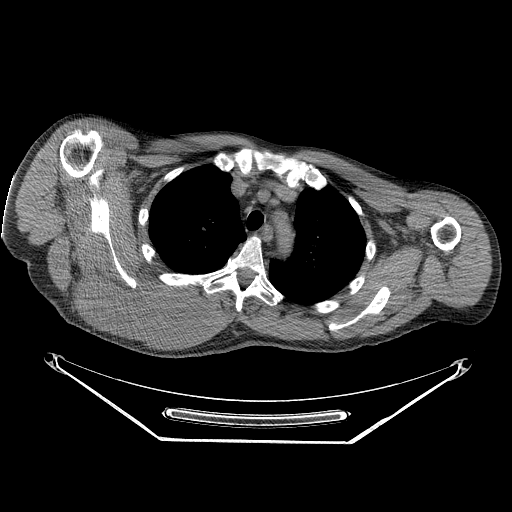
CT of an extremity soft-tissue mass (from a PET/CT study), one axial slice; slice 191 of 267 in the series (ordered by position); reconstruction kernel STANDARD; 140 kVp; soft-tissue window (W 400 / L 40 HU); 512 × 512 image matrix, field of view 500 × 500 mm. Male patient. Case-level facts recorded for this patient, not image findings: histological type: pleiomorphic spindle cell undifferentiated; grade: high; site of the primary tumour: right parascapusular.
Outlined on this slice (expert contour drawn on MRI and transferred to this co-registered scan by the dataset authors):
- gross tumour volume including surrounding oedema: bounding box <78,263,227,339> (left, top, right, bottom; pixels)
- gross tumour volume (mass): <78,263,209,336>